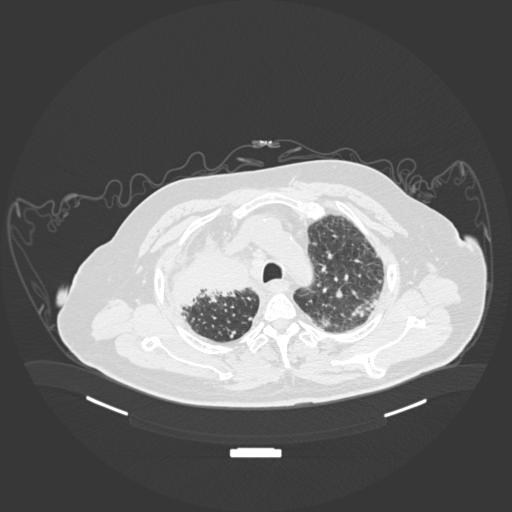
Chest CT, one axial slice. Slice 149 of 201 in the series (ordered by position). Reconstruction kernel B30f. 120 kVp. Lung window (W 1500 / L -600 HU). 1 mm slice thickness. 512 × 512 image matrix, field of view 500 × 500 mm. Patient: male, 69 years. Case-level facts recorded for this patient, not image findings: clinical TNM (as recorded): T4 N3 M1.
Structures marked on this image (bounding box drawn by a radiologist):
- lung tumour (recorded histology: adenocarcinoma): bounding box [x1, y1, x2, y2] px = [161, 228, 255, 313]